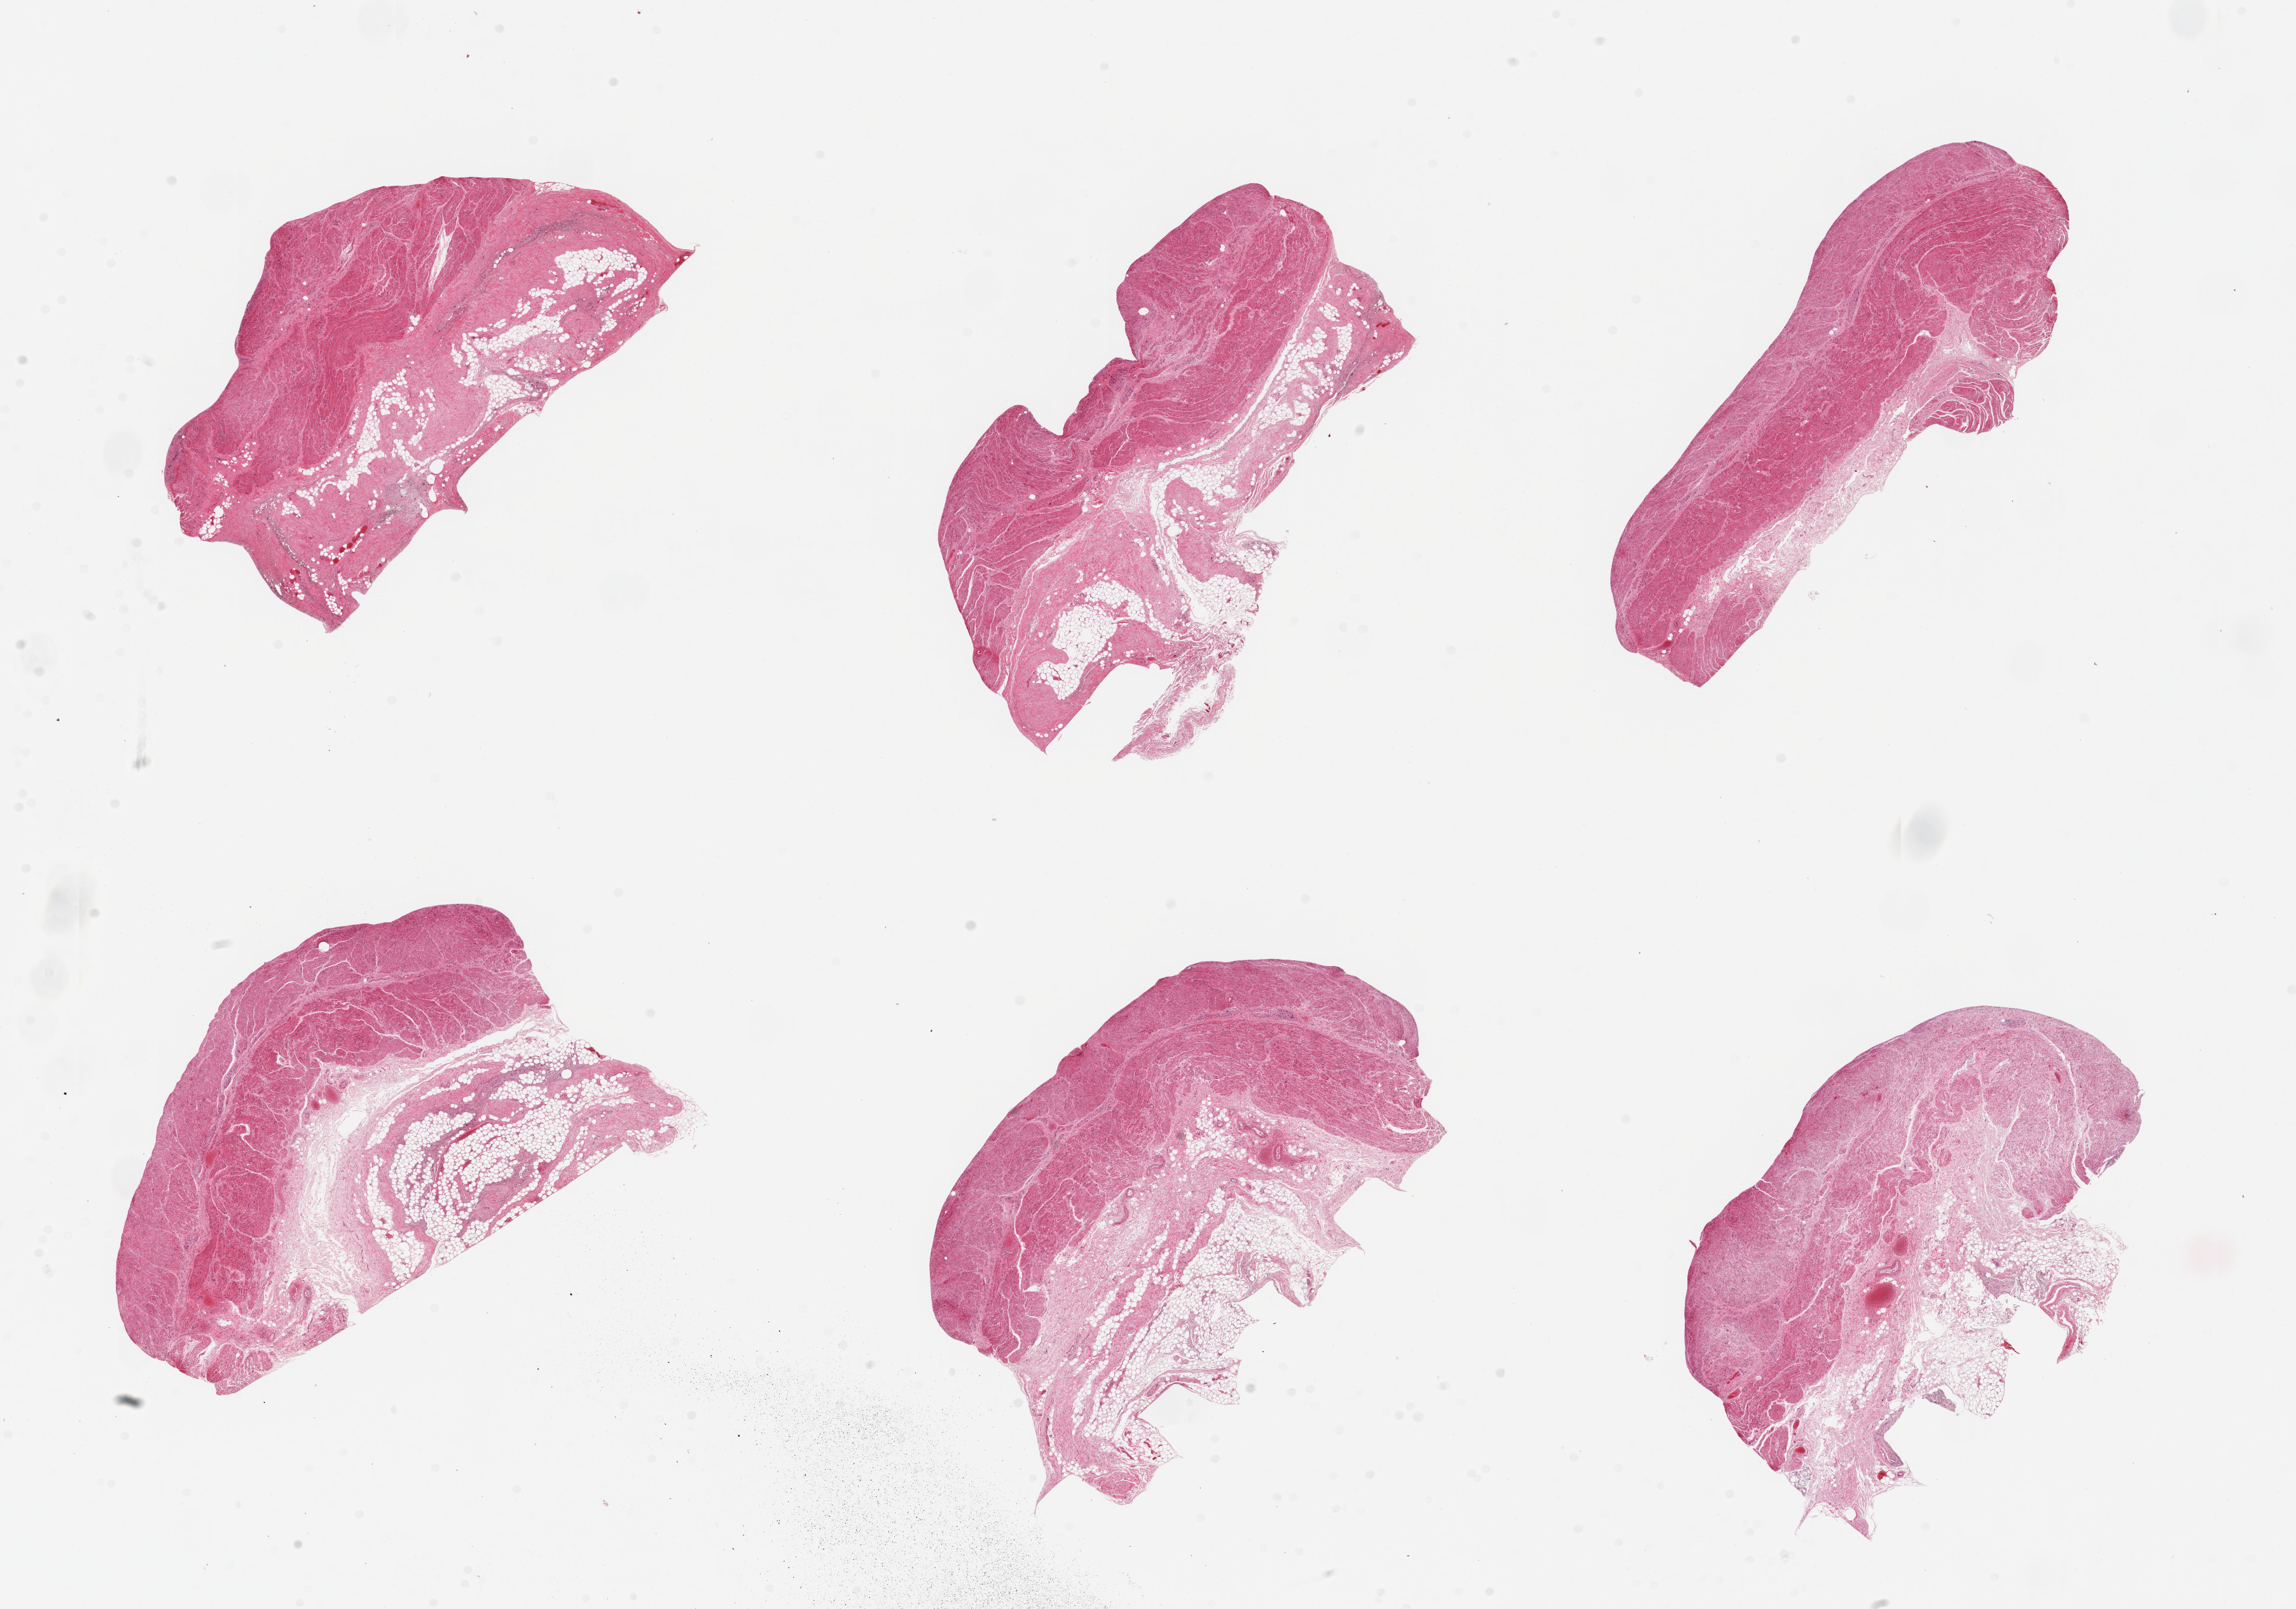
Hematoxylin and eosin (H&E) whole-slide image, whole scanned area (about 28.5 x 20.0 mm, acquisition: 20x scan) shown as a low-resolution overview. PAXgene-fixed paraffin-embedded (PFPE) section. Section of gastroesophageal junction (target tissue). Tissue donor sample. Donor sex: male.
* review note (as recorded): 6 pieces; up to 2 mm perimuscular fibroadipose tissue